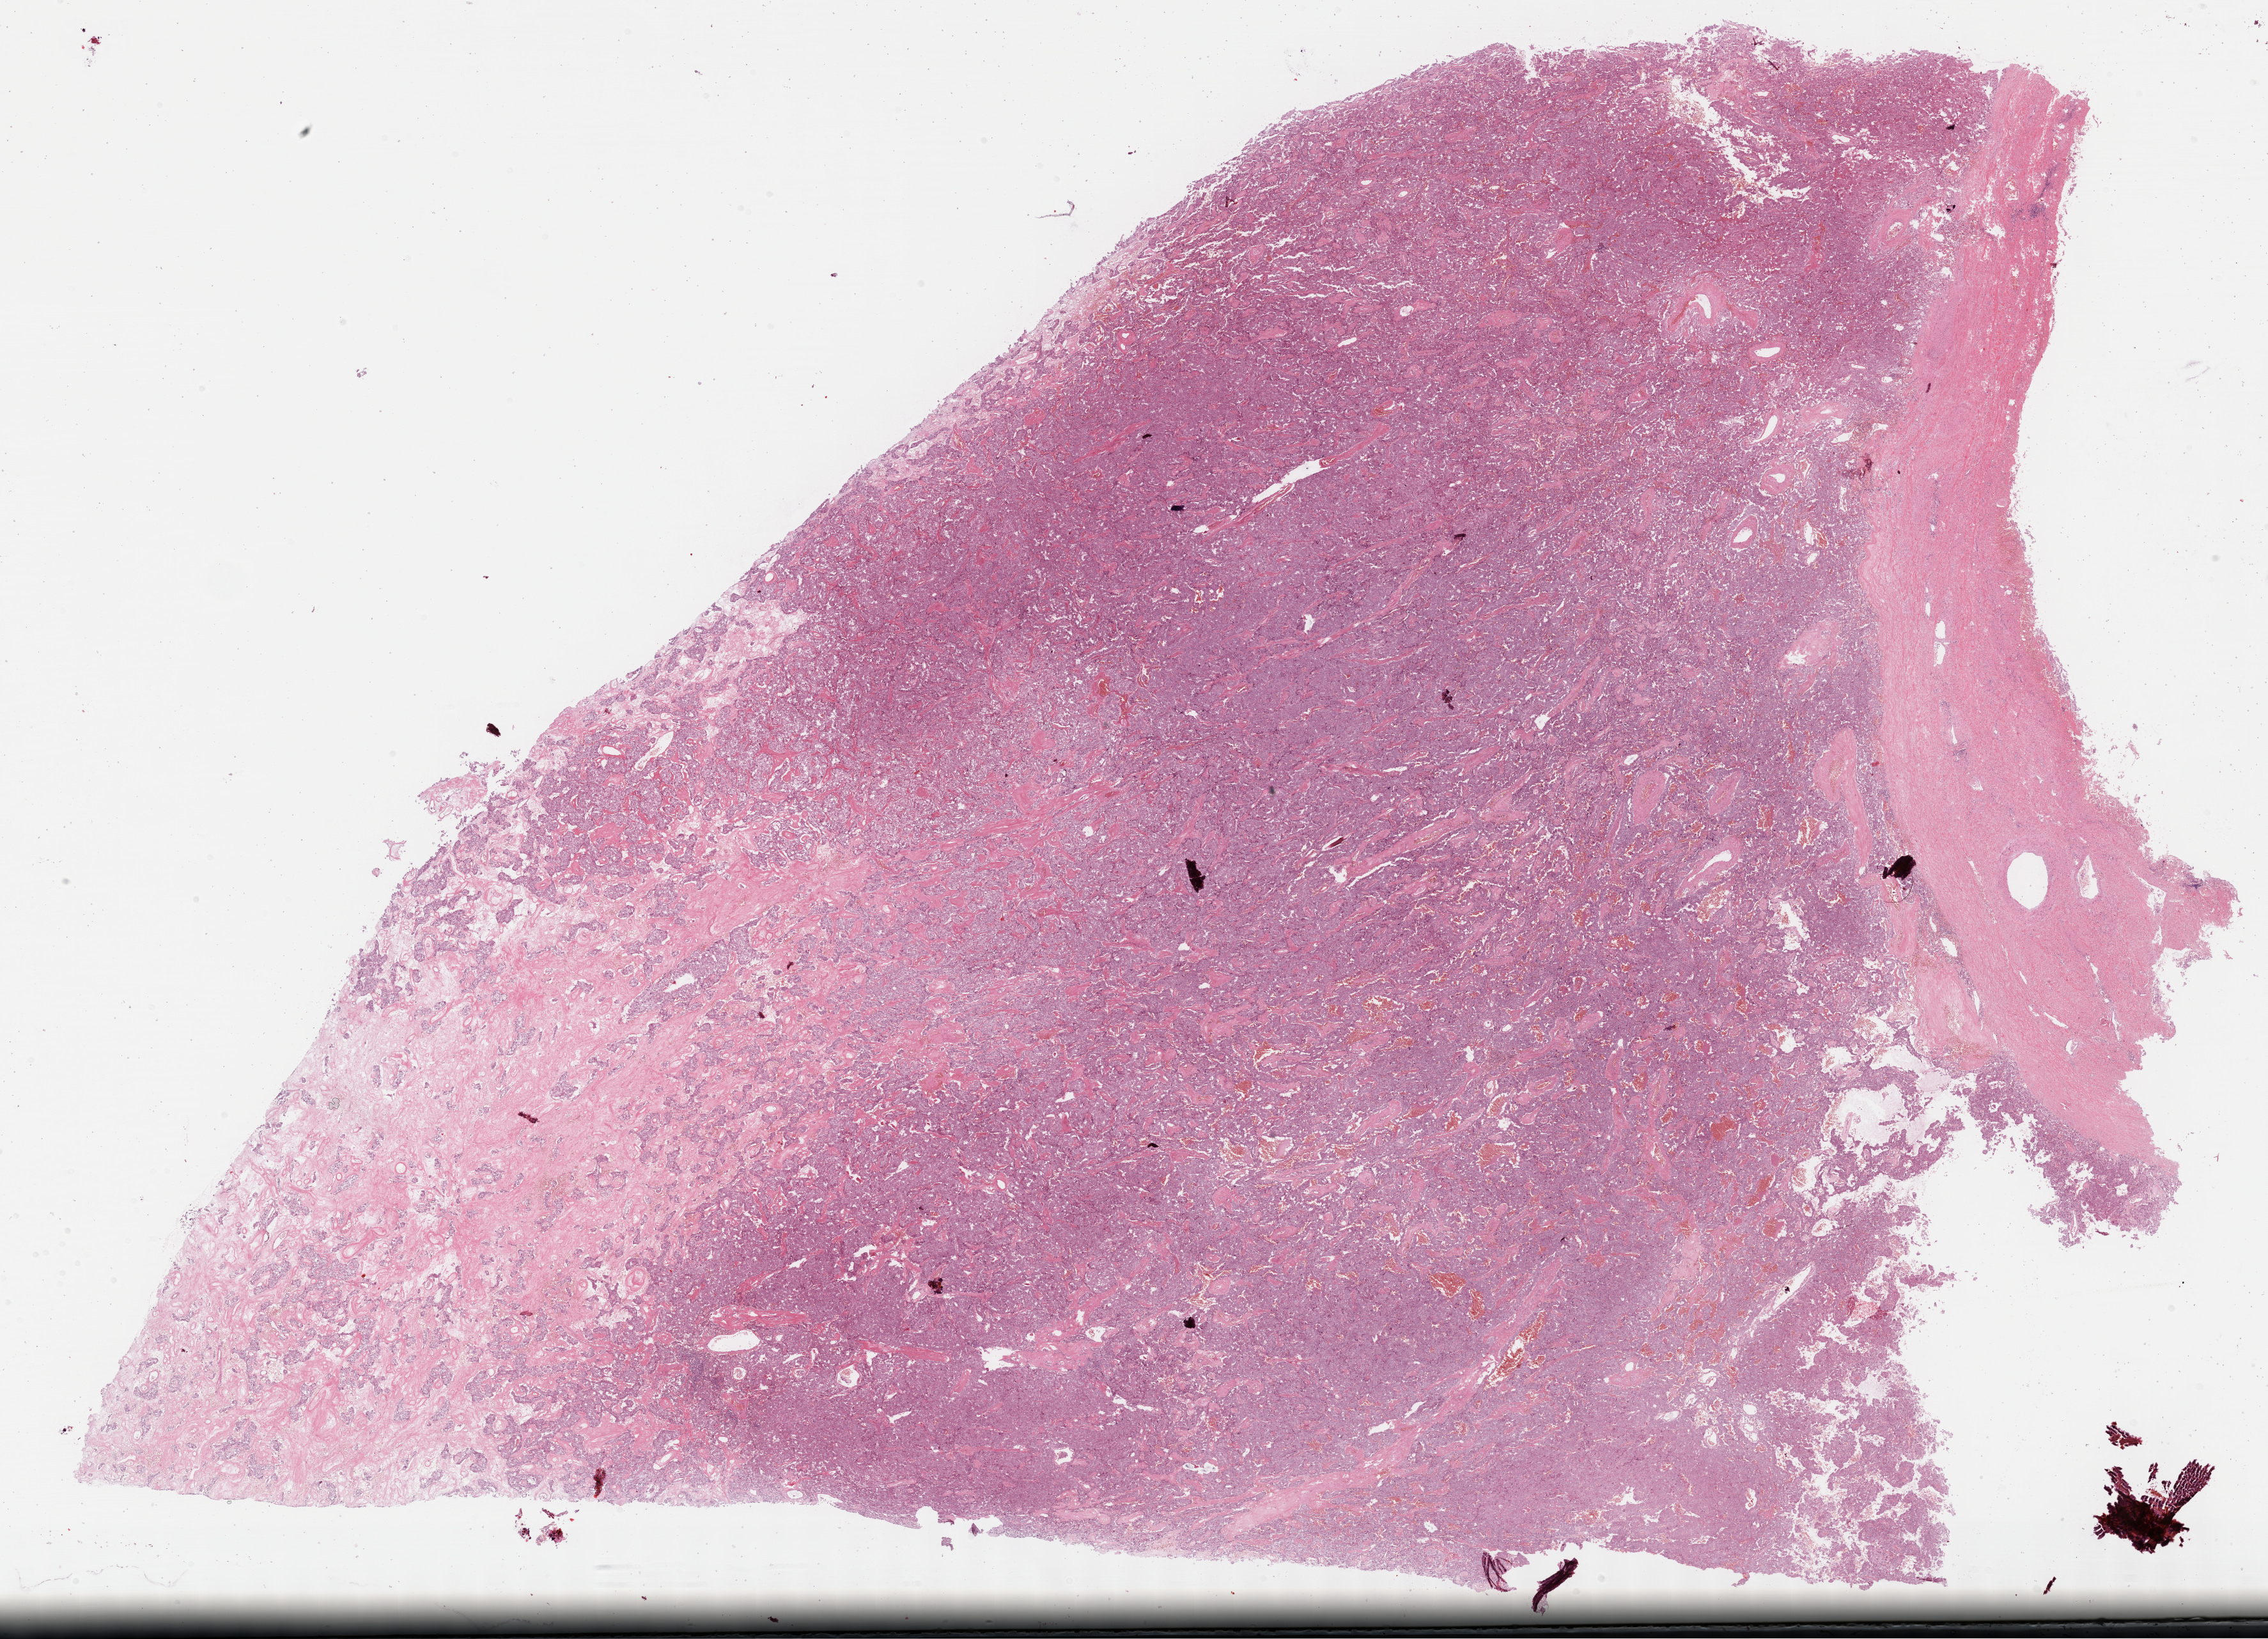
Digitized H&E-stained tissue section (whole slide) — low-resolution overview of the scanned area, about 28.7 x 20.7 mm; formalin-fixed paraffin-embedded (FFPE) diagnostic section; adrenal gland, primary tumour sample. Male, age 59 years at initial diagnosis.
Histologic diagnosis: Pheochromocytoma, malignant.